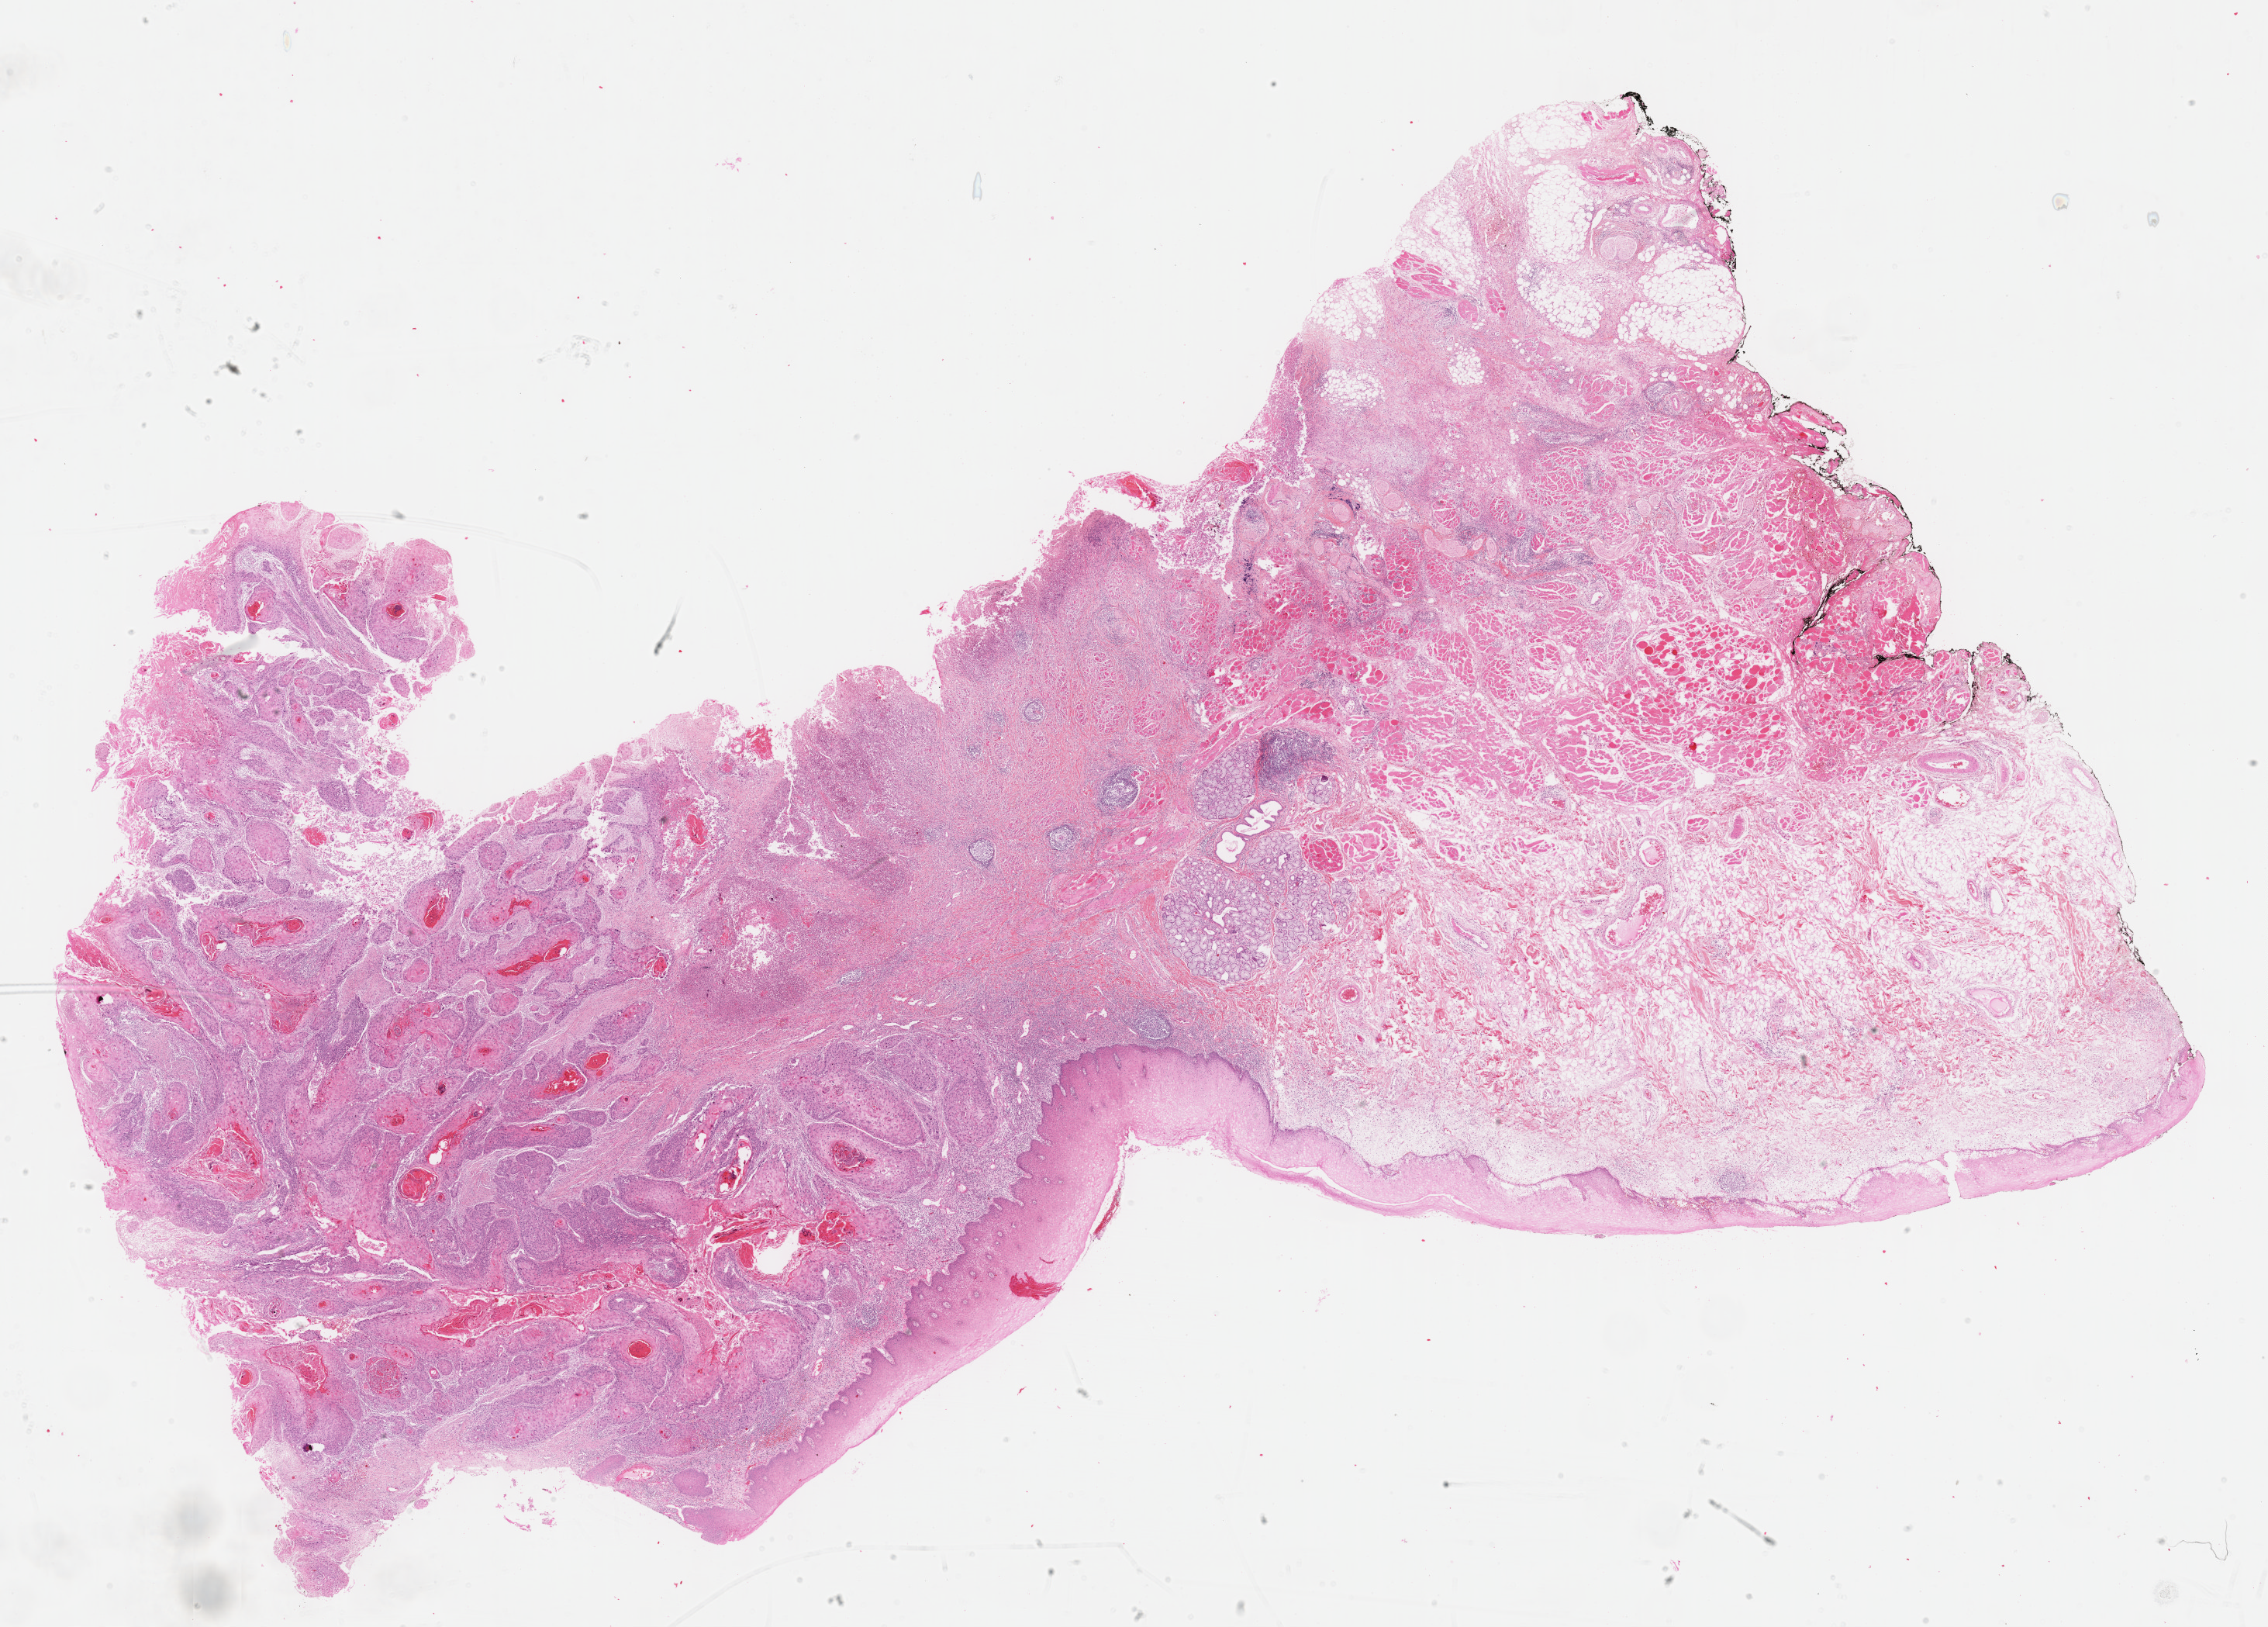
H&E whole-slide image — a low-resolution overview of the entire scanned area, about 23.6 x 17.0 mm. Formalin-fixed paraffin-embedded (FFPE) diagnostic section. Primary tumour sample from the head and neck. Male, age 59 years at initial diagnosis.
Diagnosis: Squamous cell carcinoma, NOS (mouth, NOS).